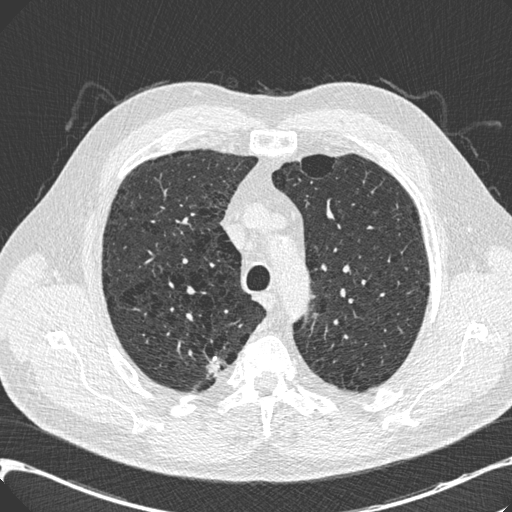
Low-dose screening chest CT, one axial slice; position 151 of 197 along the scan axis; reconstruction kernel B30f; 120 kVp; lung window (W 1500 / L -600 HU); 0.75 mm slice thickness; 512 × 512 image matrix, field of view 367 × 367 mm.
Structures marked on this image (manually delineated by an expert):
- lesion 1 (tumor, upper lobe of right lung): bounding box <207,355,222,377> (left, top, right, bottom; pixels)